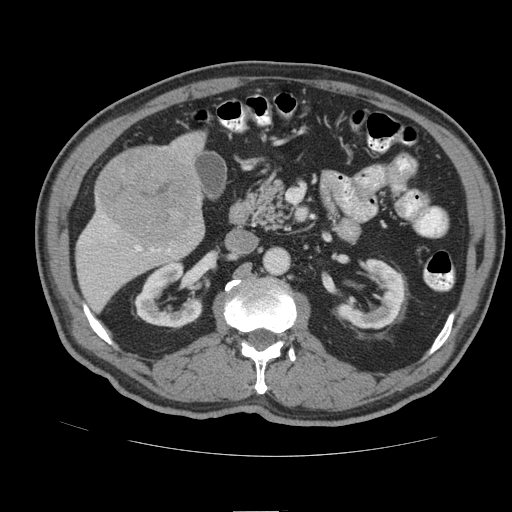
Contrast-enhanced abdominal CT (liver protocol), one axial slice. Position 37 of 105 along the scan axis. Reconstruction kernel STANDARD. Soft-tissue window (W 400 / L 40 HU). 2.5 mm slice thickness. 512 × 512 image matrix. Case-level facts recorded for this patient, not image findings: diagnosis: hepatocellular carcinoma (patient treated with transarterial chemoembolisation; whether this scan precedes or follows treatment is not stated here); TNM stage (as recorded): Stage-IIIB; Child-Pugh class: A; tumour nodularity: multinodular.
Structures marked on this image (semi-automatically segmented with operator editing):
- liver parenchyma outside the tumour (the mass and vessels are separate outlines, so this box may not span the whole liver): bounding box [x1, y1, x2, y2] px = [76, 130, 206, 310]
- mass: [98, 149, 199, 245]
- liver vessels: [104, 222, 170, 252]